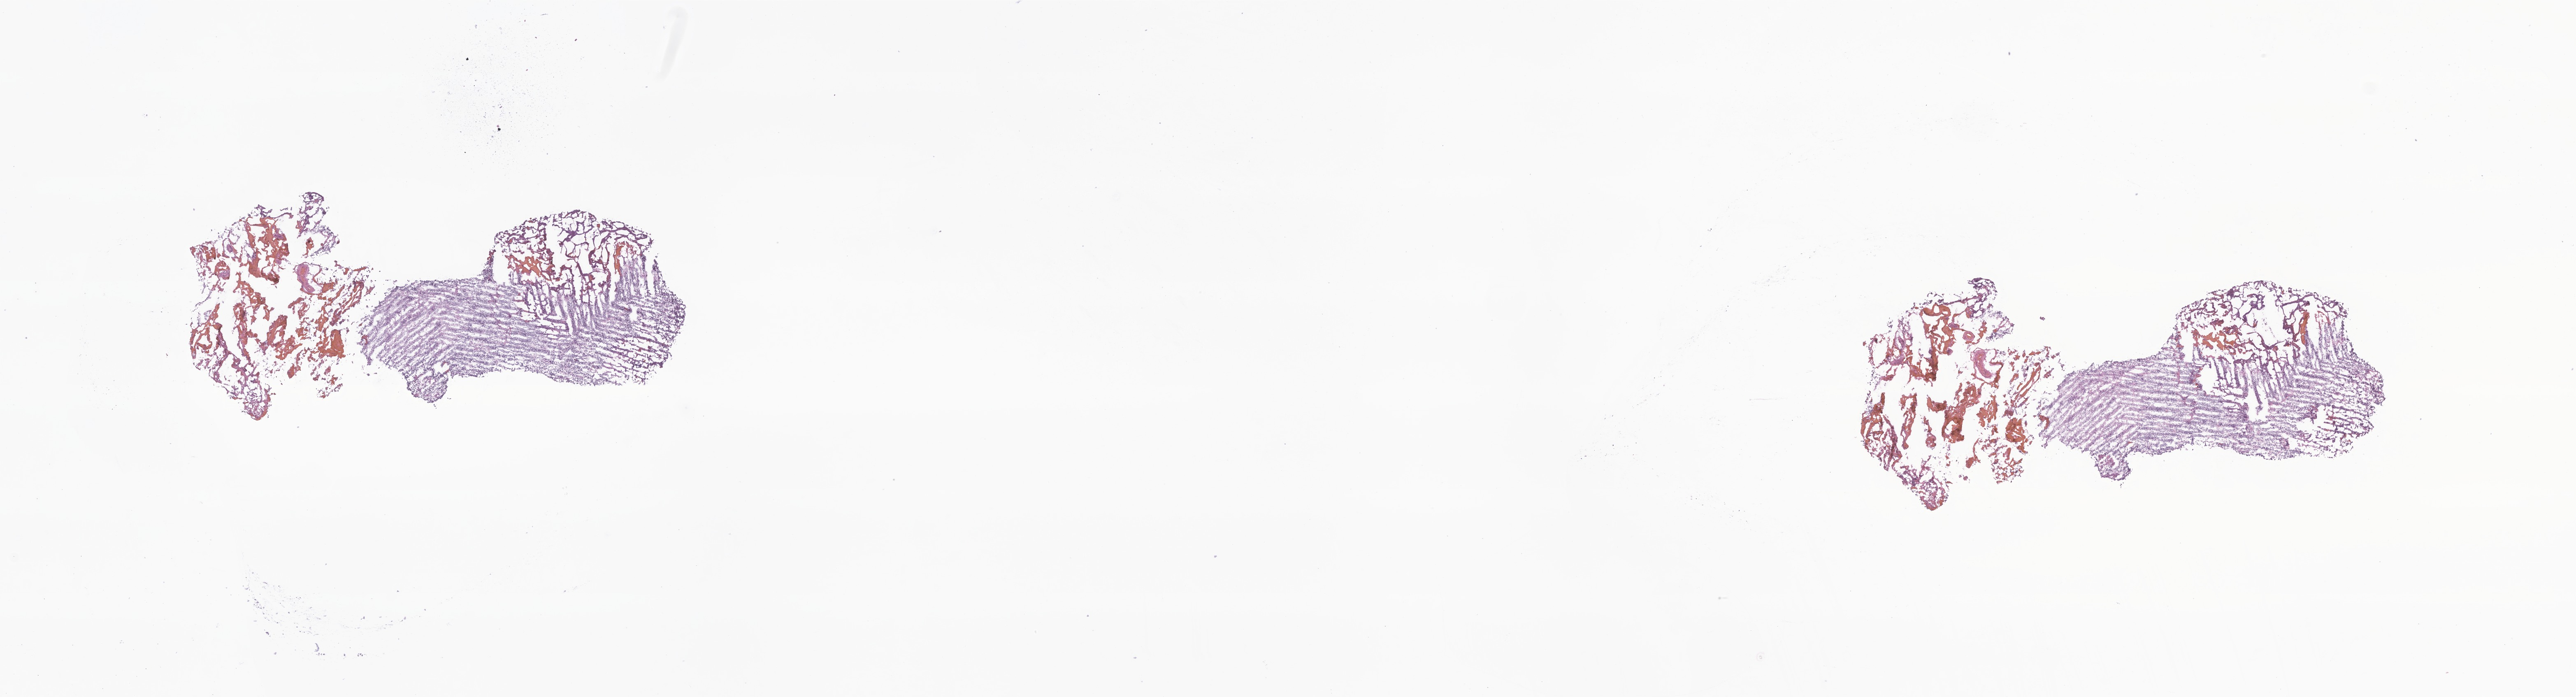
Hematoxylin and eosin (H&E) whole-slide image of tumor tissue from the brain — a low-resolution overview of the entire scanned area, about 26.4 x 7.1 mm, frozen section. Patient: male, age 208 months (17 years 4 months).
Recorded diagnosis: Medulloblastoma, NOS.